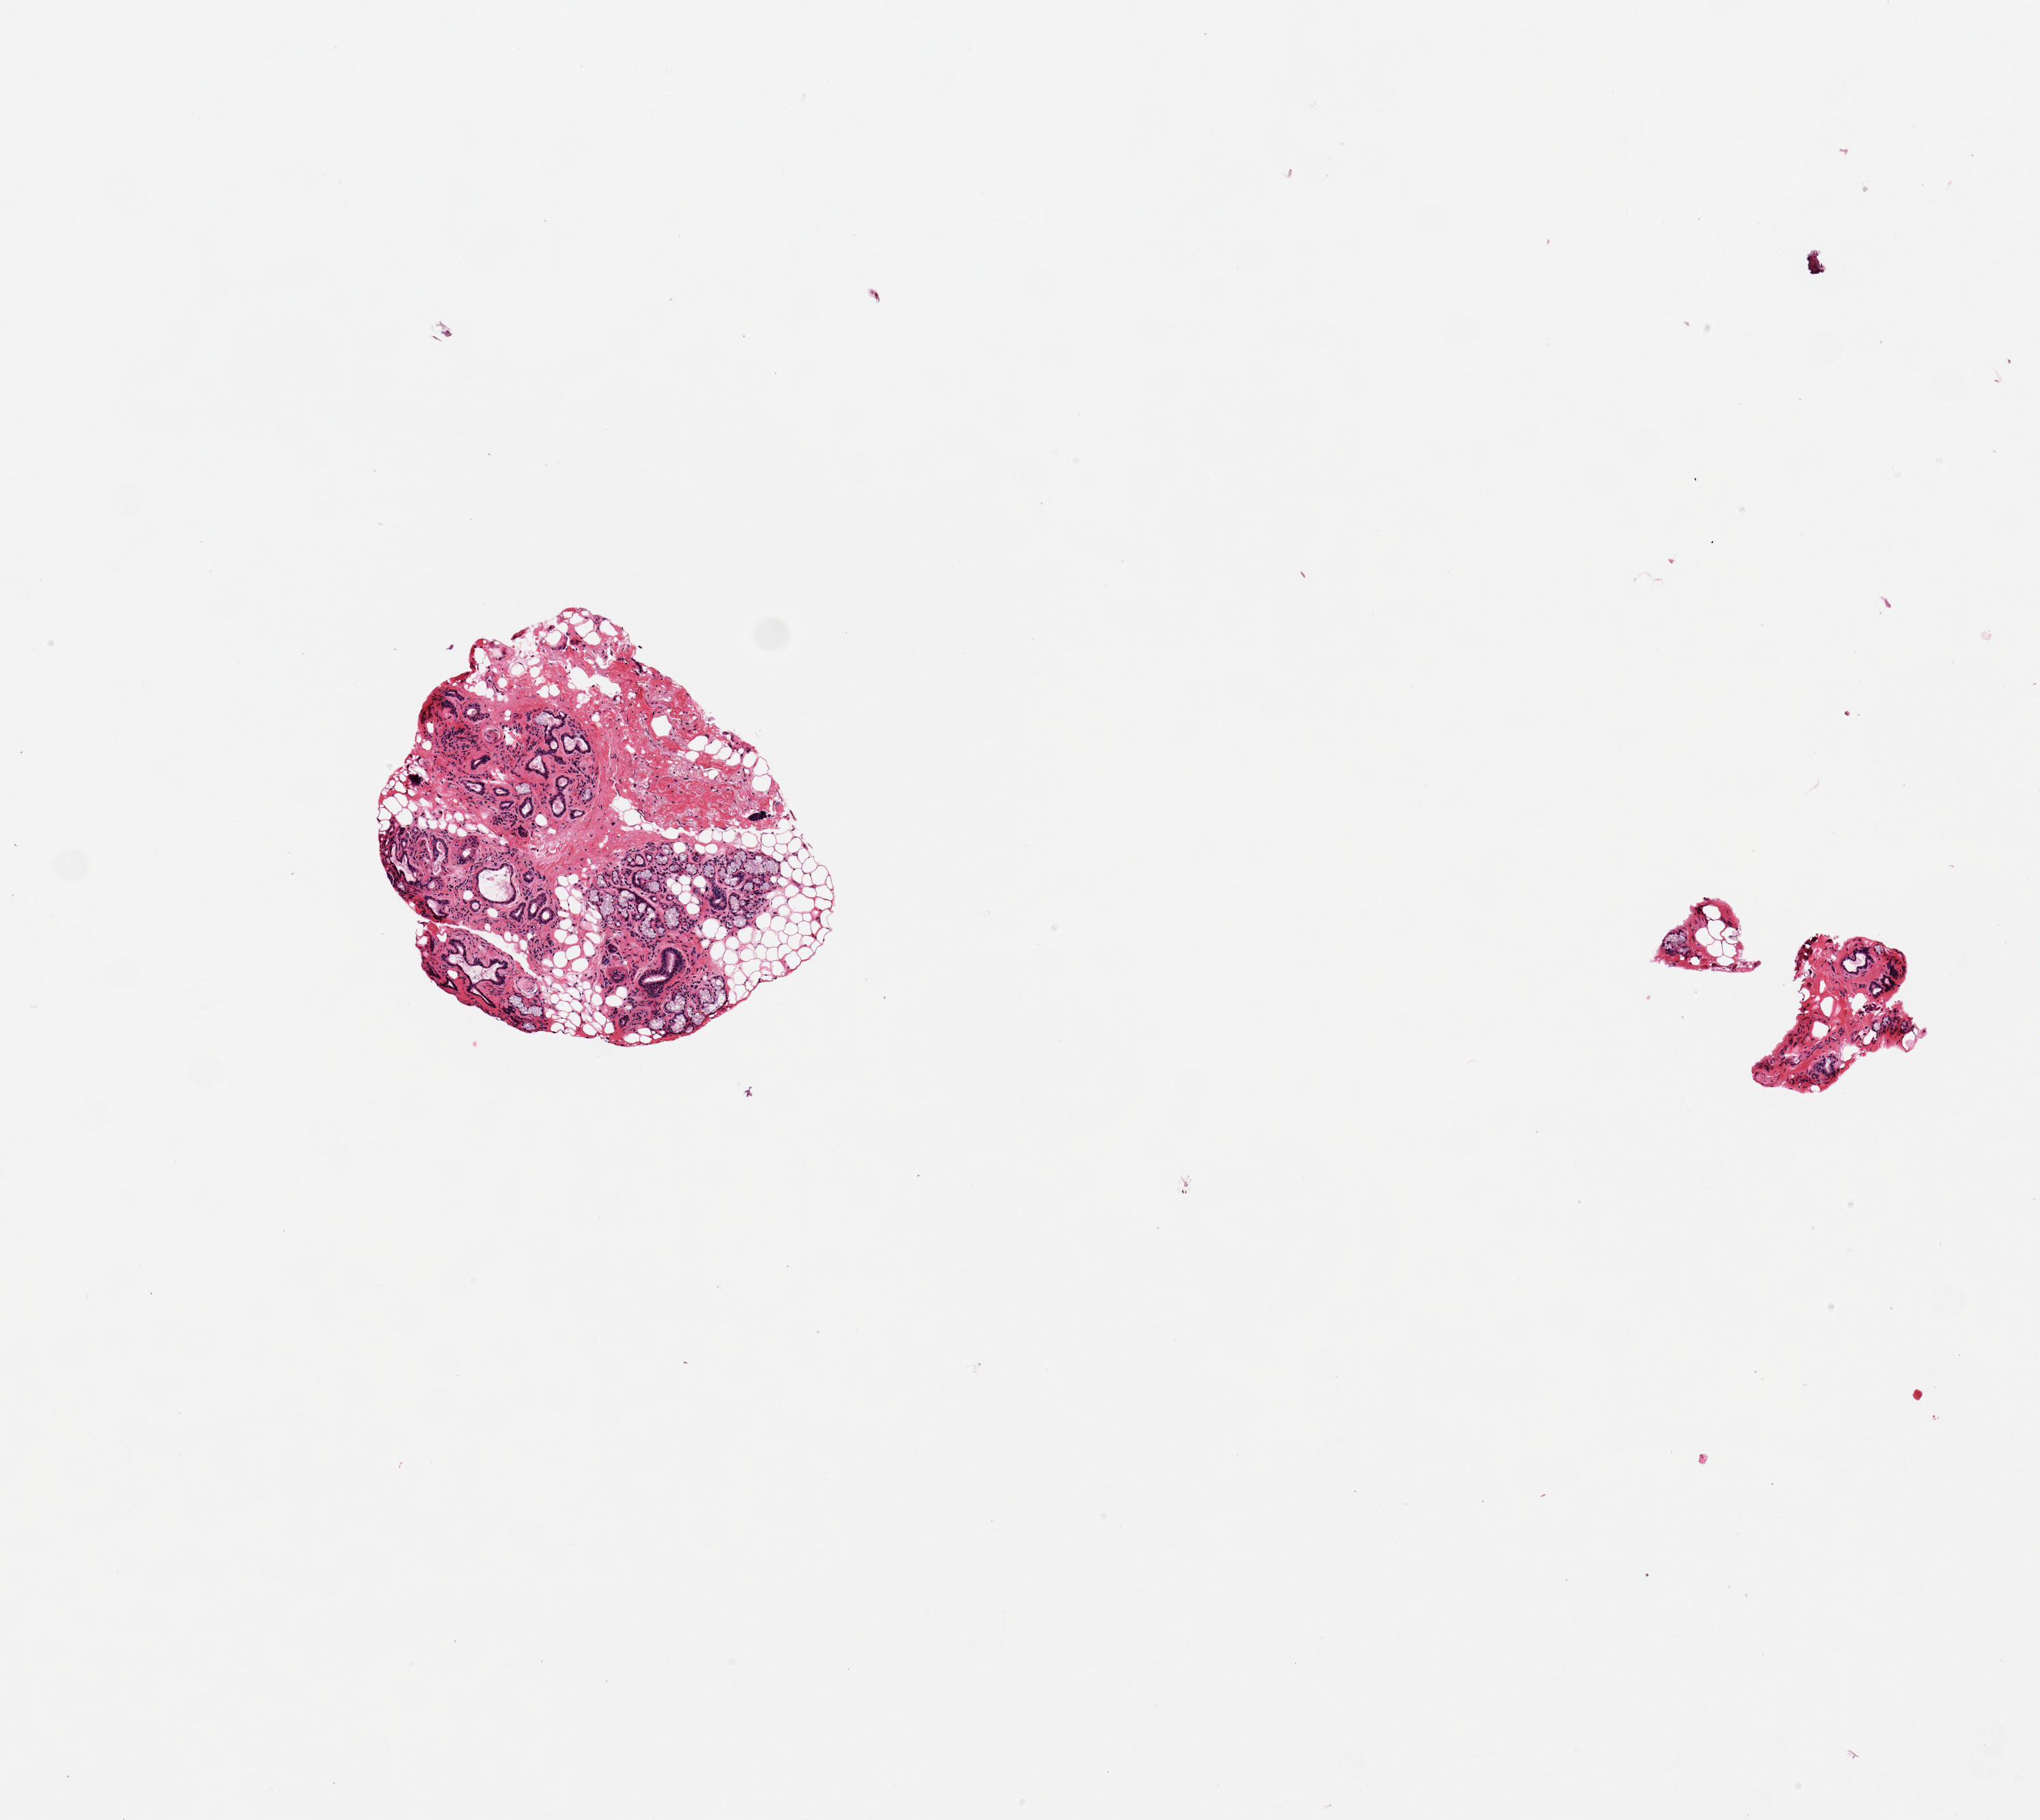
Whole-slide image, haematoxylin and eosin stain — a low-resolution overview of the entire scanned area, about 5.9 x 5.3 mm. PAXgene-fixed paraffin-embedded (PFPE) section. Sampled site (target tissue): minor salivary gland. Tissue donor sample. Female donor.
* pathologist's review note for this sample: 1 piece + minute fragement; ~40% glandular tissue, rest is fibrotic + adipose tissue